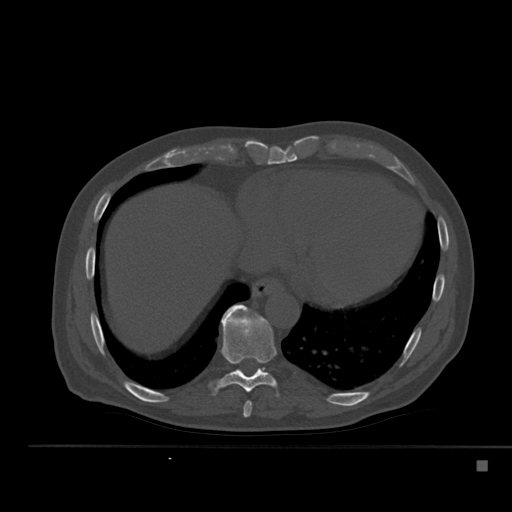
CT including the spine, one axial slice; slice 287 of 517 in the series (ordered by position); 120 kVp; bone window (W 1800 / L 400 HU); 1.5 mm slice thickness; 512 × 512 image matrix. Male patient, age 70 years. Case-level facts recorded for this patient, not image findings: primary cancer: renal.
Structures marked on this image (semi-automatically segmented with operator editing):
- T10 vertebra: bounding box (x1, y1, x2, y2) in pixels: (227, 307, 264, 376)
- T8 vertebra: (243, 401, 252, 418)
- T9 vertebra: (209, 305, 279, 396)